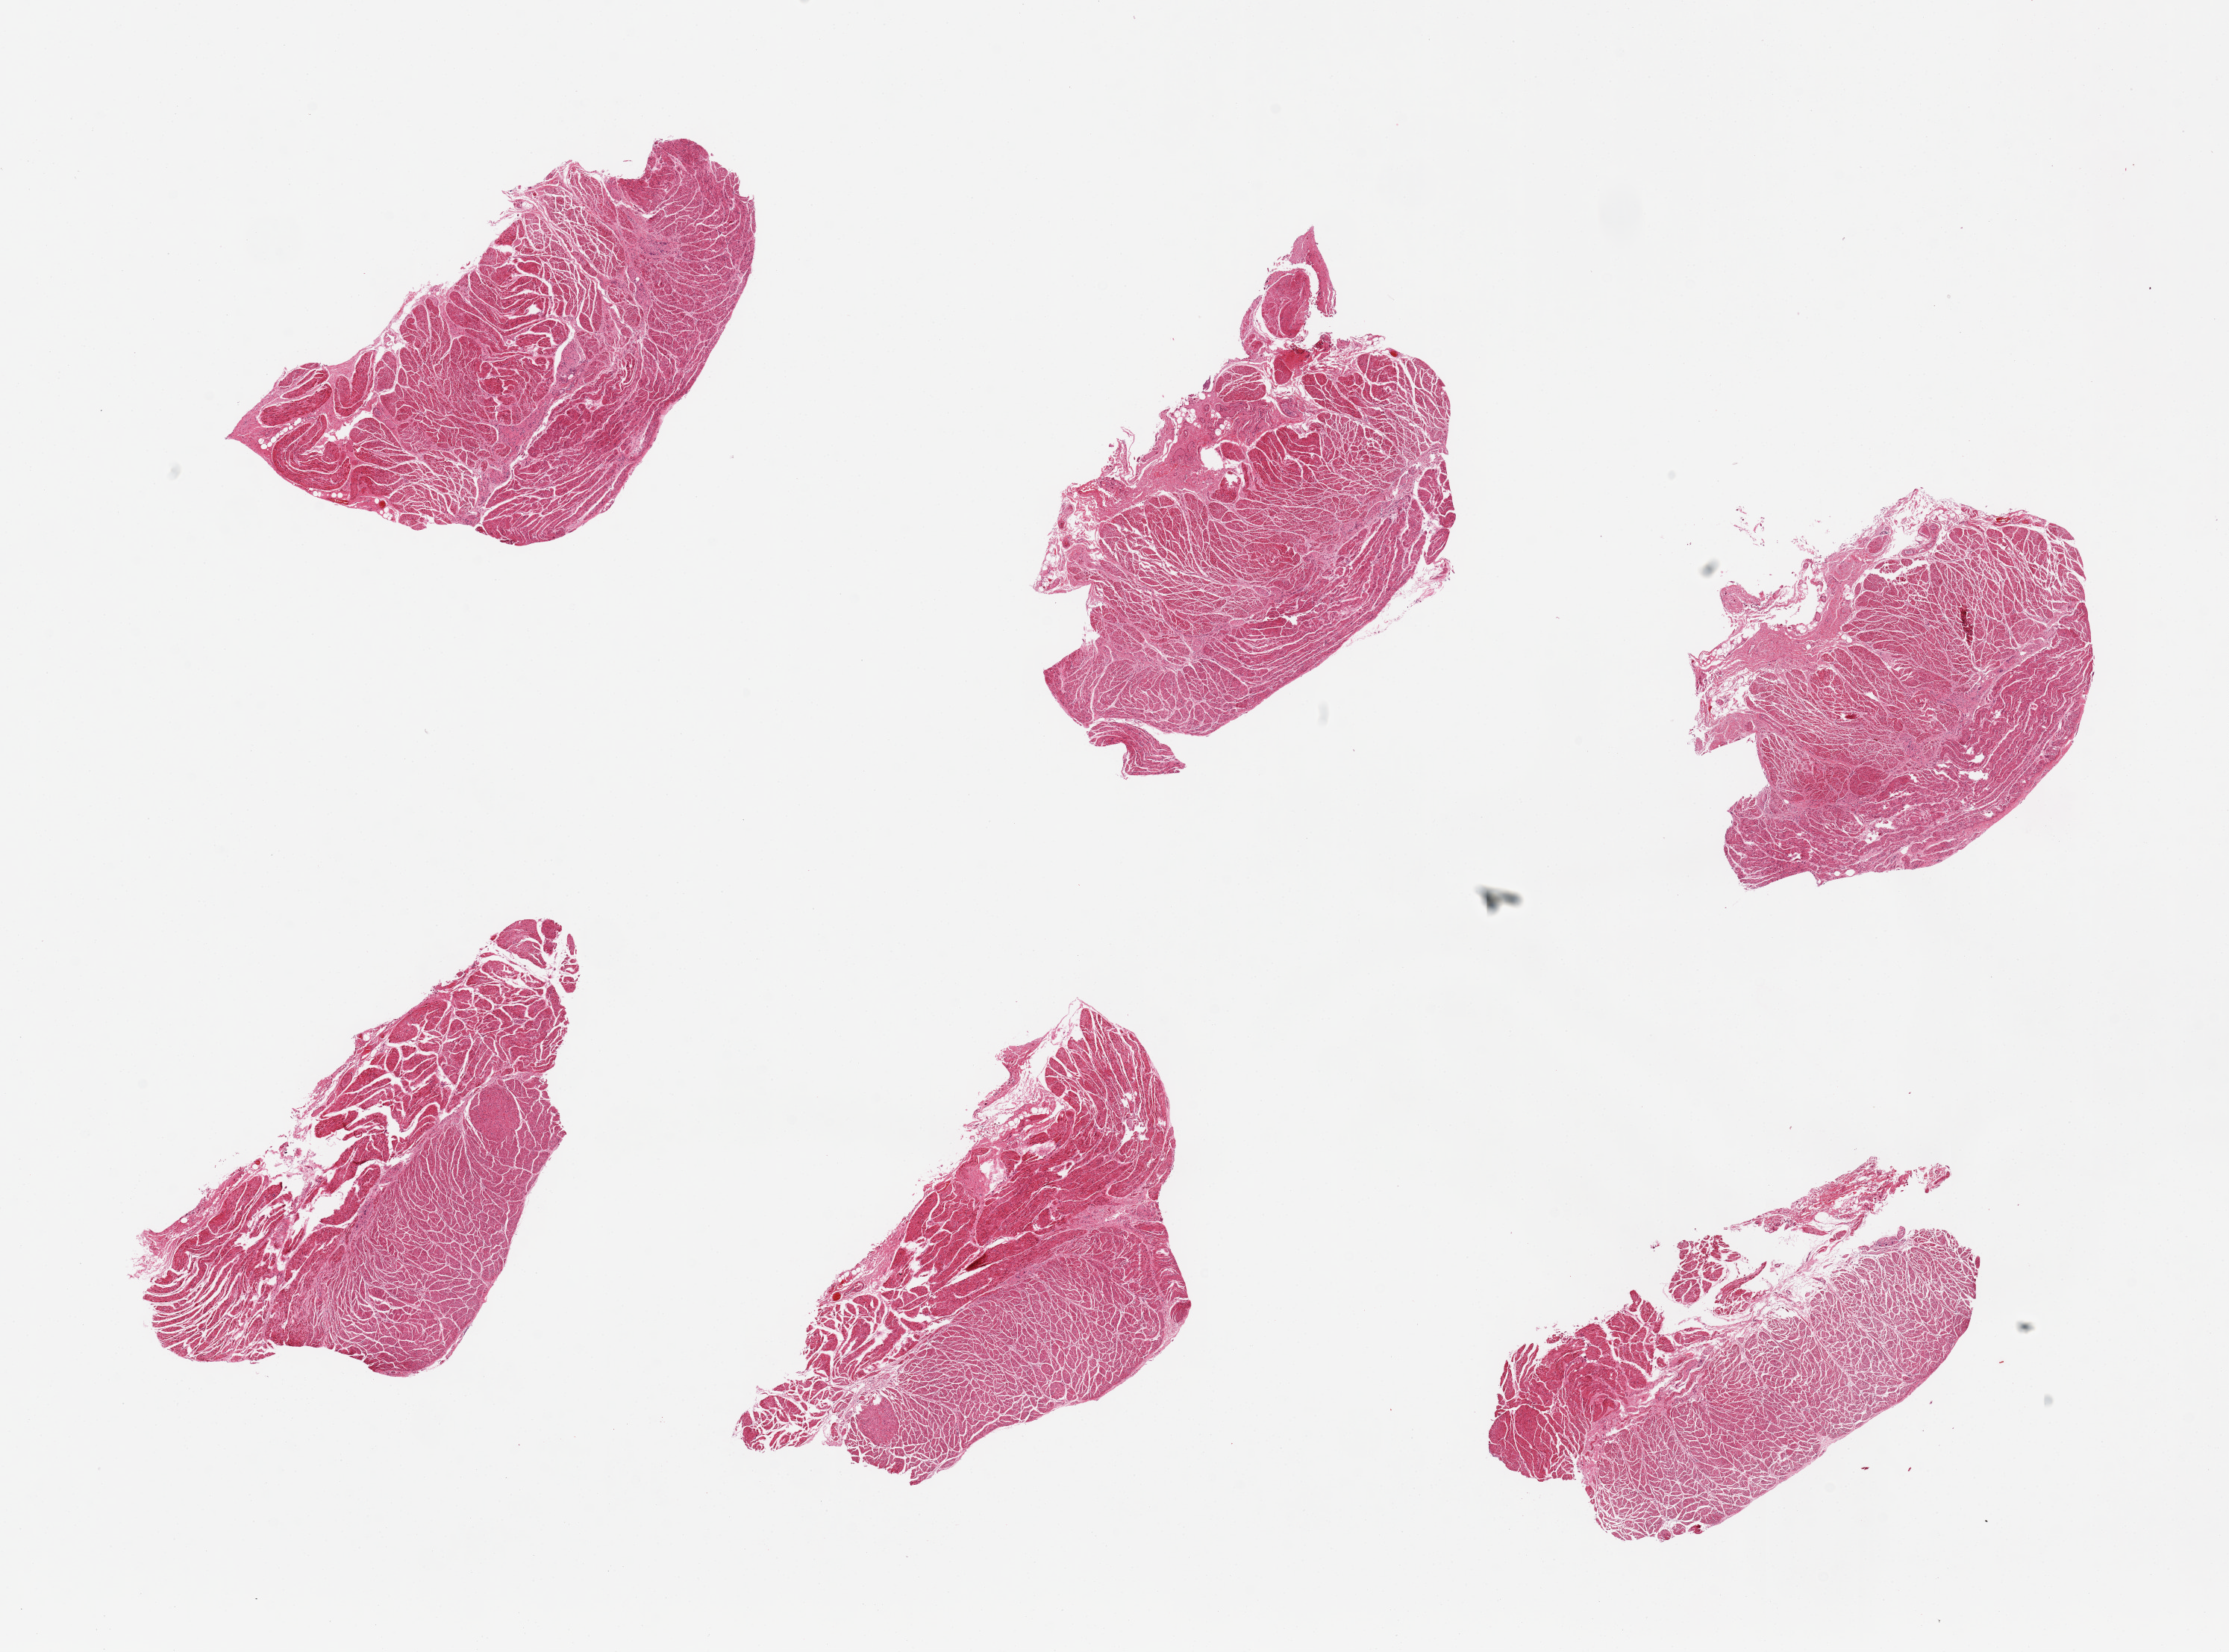
Whole-slide image, H&E stain — low-resolution overview of the scanned area, about 23.6 x 17.5 mm (slide scanned at 20x), PAXgene-fixed paraffin-embedded (PFPE) section, sampled site (target tissue): gastroesophageal junction, tissue donor sample.
- review note (as recorded): 6 pieces, well trimmed